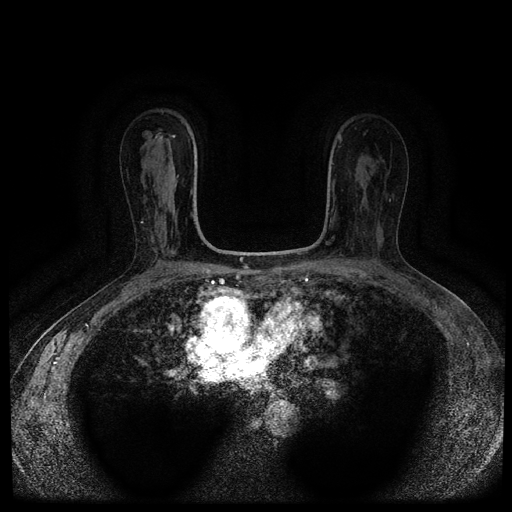
Breast MRI (dynamic contrast-enhanced, multi-phase), one axial slice. Position 63 of 116 along the scan axis. Dynamic contrast-enhanced series, time point 2 of 5 at this slice position (early post-contrast). 1.5 T. TE 2.7 ms, TR 5.4 ms. 2 mm slice thickness. 512 × 512 image matrix. Patient: female, 63 years.
Outlined on this slice (semi-automatically segmented with operator editing):
- breast lesion (labelled benign in the annotation): bounding box (x1, y1, x2, y2) in pixels: (143, 131, 153, 139)